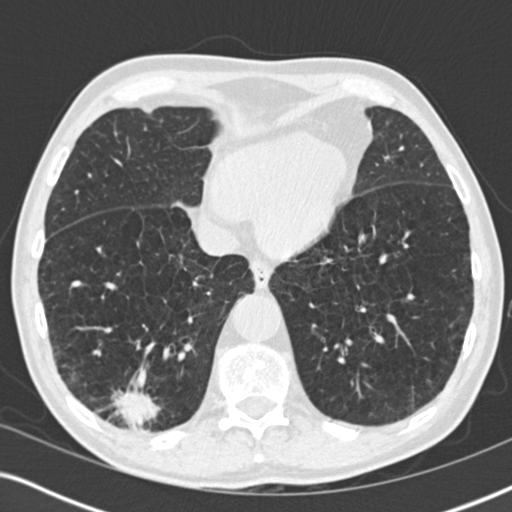
Low-dose screening chest CT, one axial slice. Slice 61 of 196 in the series (ordered by position). 120 kVp. Lung window (W 1500 / L -600 HU). 2 mm slice thickness. 512 × 512 image matrix.
Structures marked on this image (outlined manually by an expert reader):
- lesion 3 (tumor, lower lobe of right lung): bounding box [x1, y1, x2, y2] px = [113, 387, 159, 429]